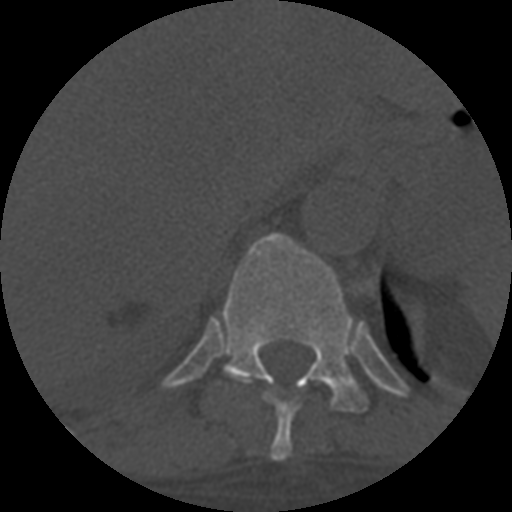
CT including the spine, one axial slice. Position 344 of 708 along the scan axis. 120 kVp. One of 3 acquisitions stored at this slice position. Bone window (W 1800 / L 400 HU). 1.25 mm slice thickness. 512 × 512 image matrix, field of view 160 × 160 mm. Patient age 55 years. Case-level facts recorded for this patient, not image findings: primary cancer: colon; vertebrae with lytic lesions (as recorded): T12, L1, L5.
Annotated regions visible in this slice (semi-automatically segmented with operator editing):
- T10 vertebra: bounding box <228,373,299,461> (left, top, right, bottom; pixels)
- T11 vertebra: <222,235,368,413>